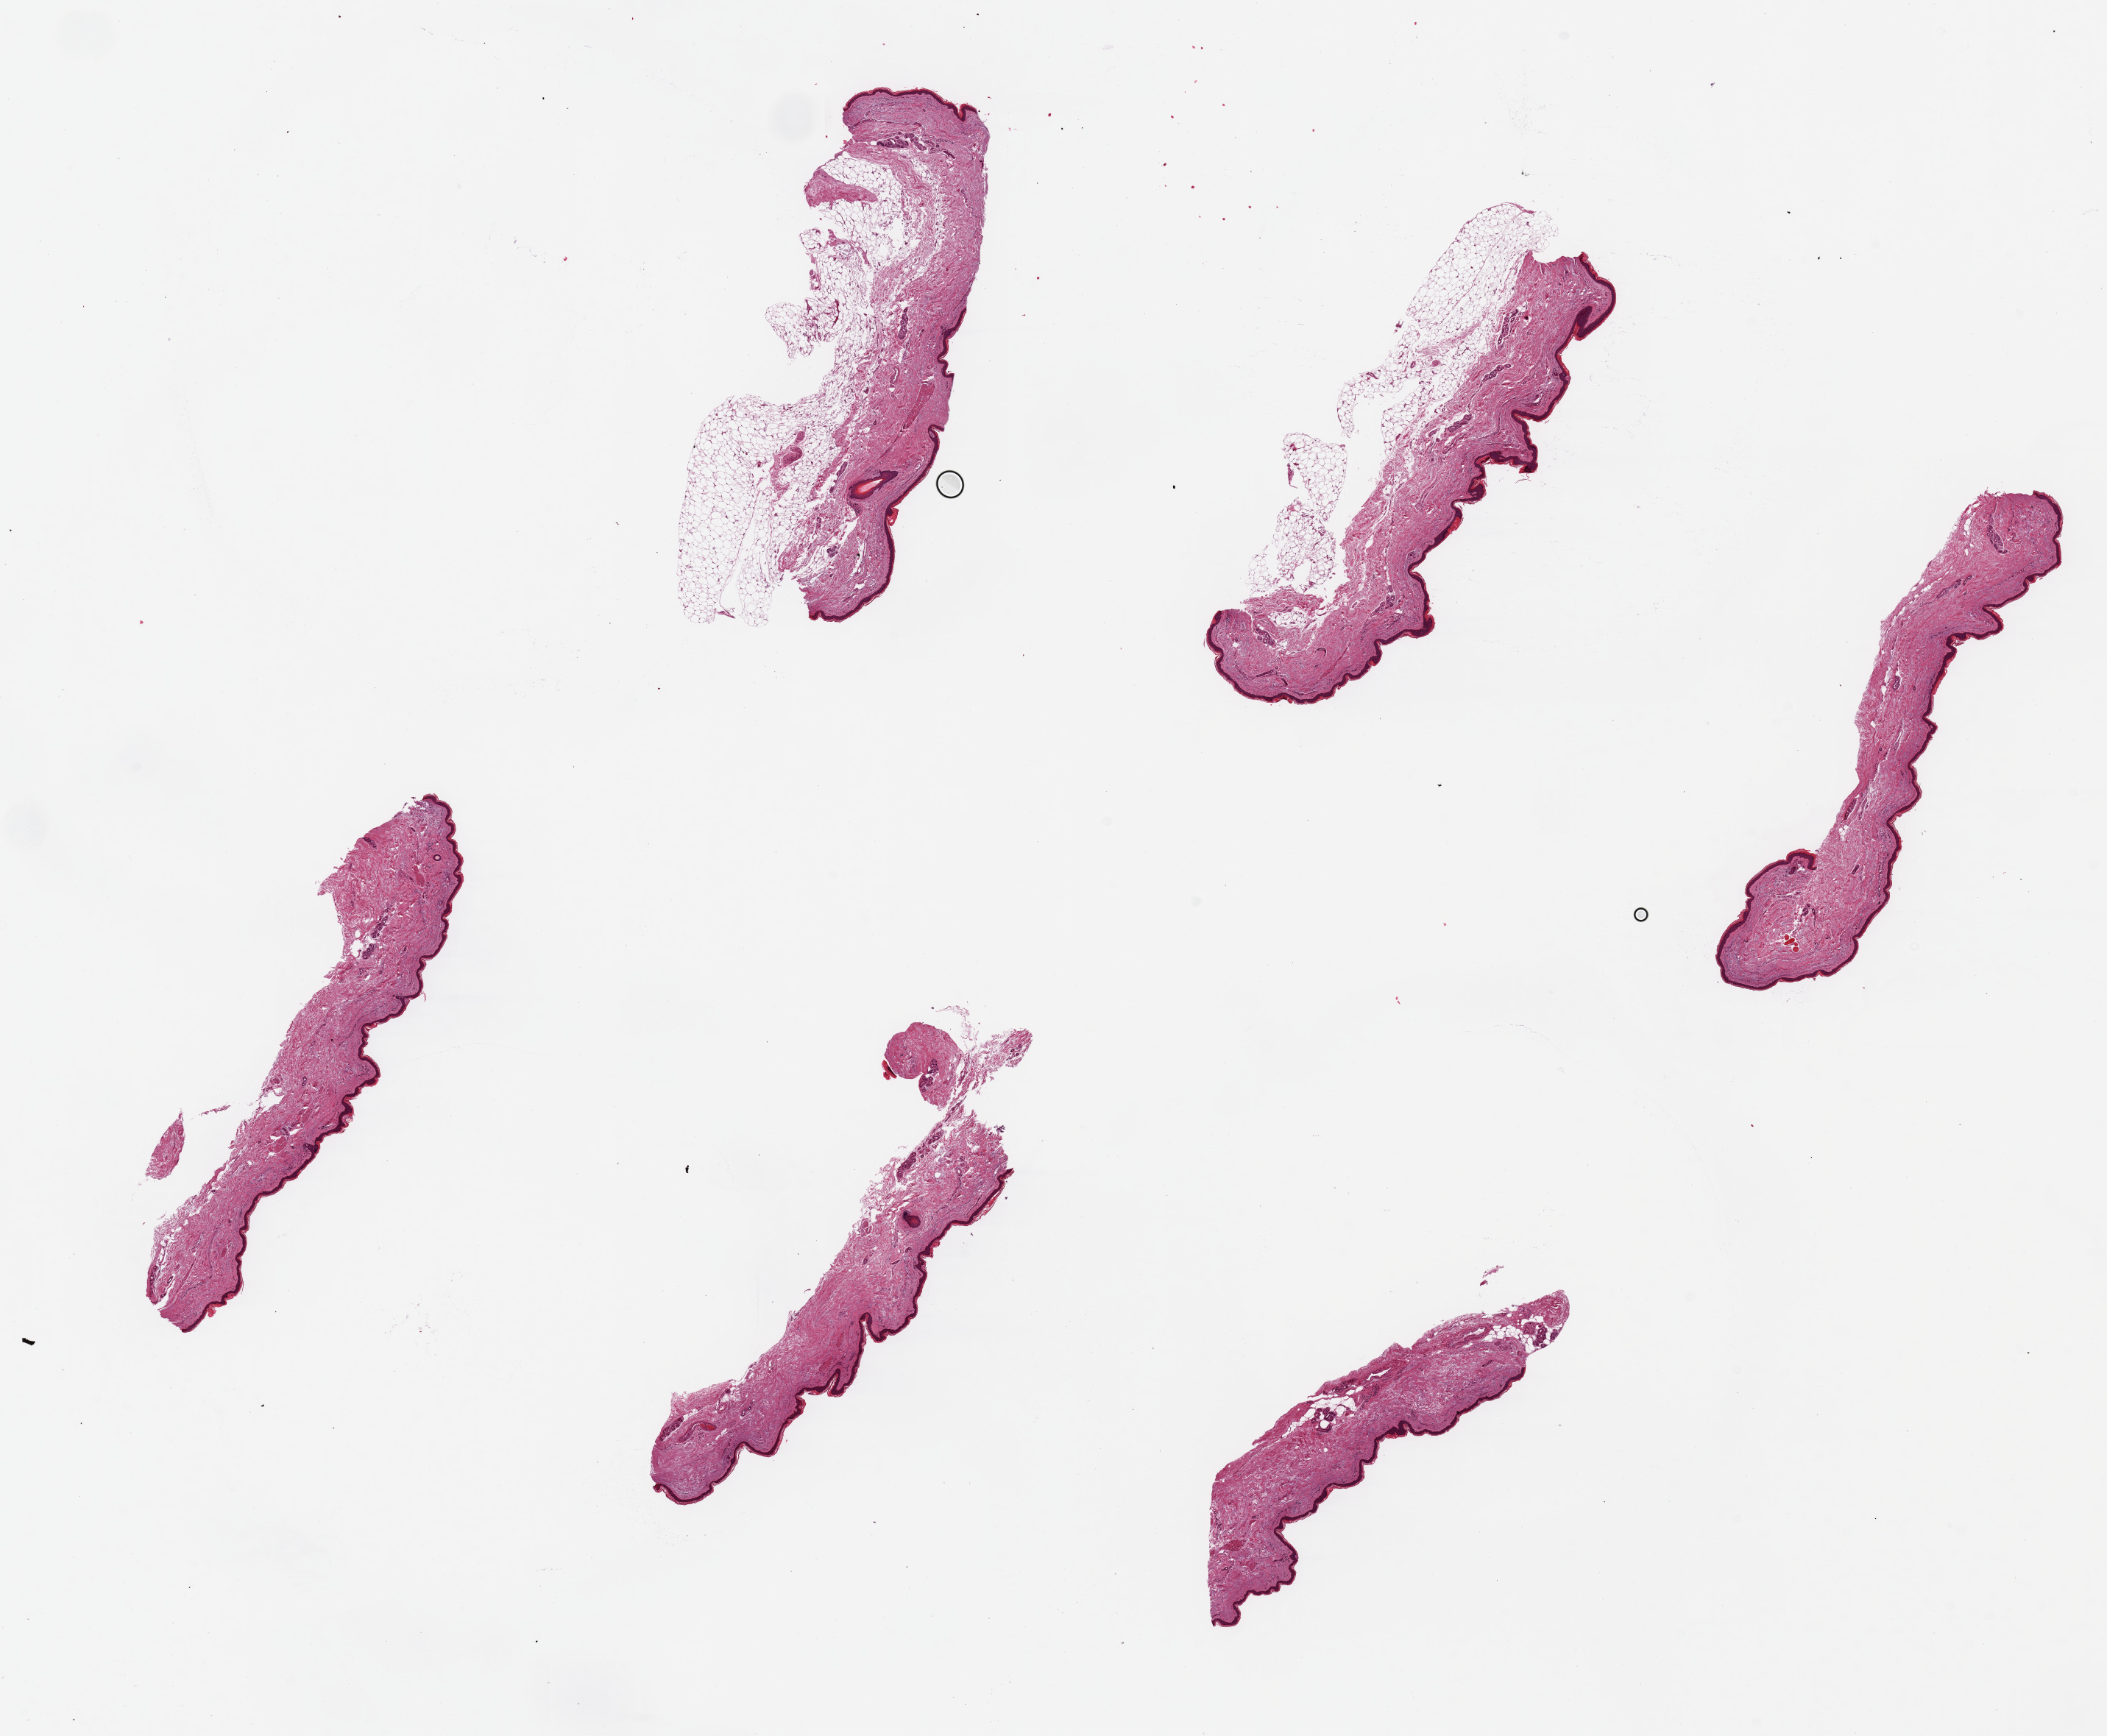
Whole-slide image, hematoxylin and eosin (H&E) stain, a low-resolution overview of the entire scanned area, about 22.6 x 18.7 mm. PAXgene-fixed paraffin-embedded (PFPE) section. Section of skin of lower leg (target tissue). Tissue donor sample. Donor sex: male.
* pathologist's review note for this sample: 6 pieces; up to 6x1mm; 2 have subcutaneous adipose up to 1 mm